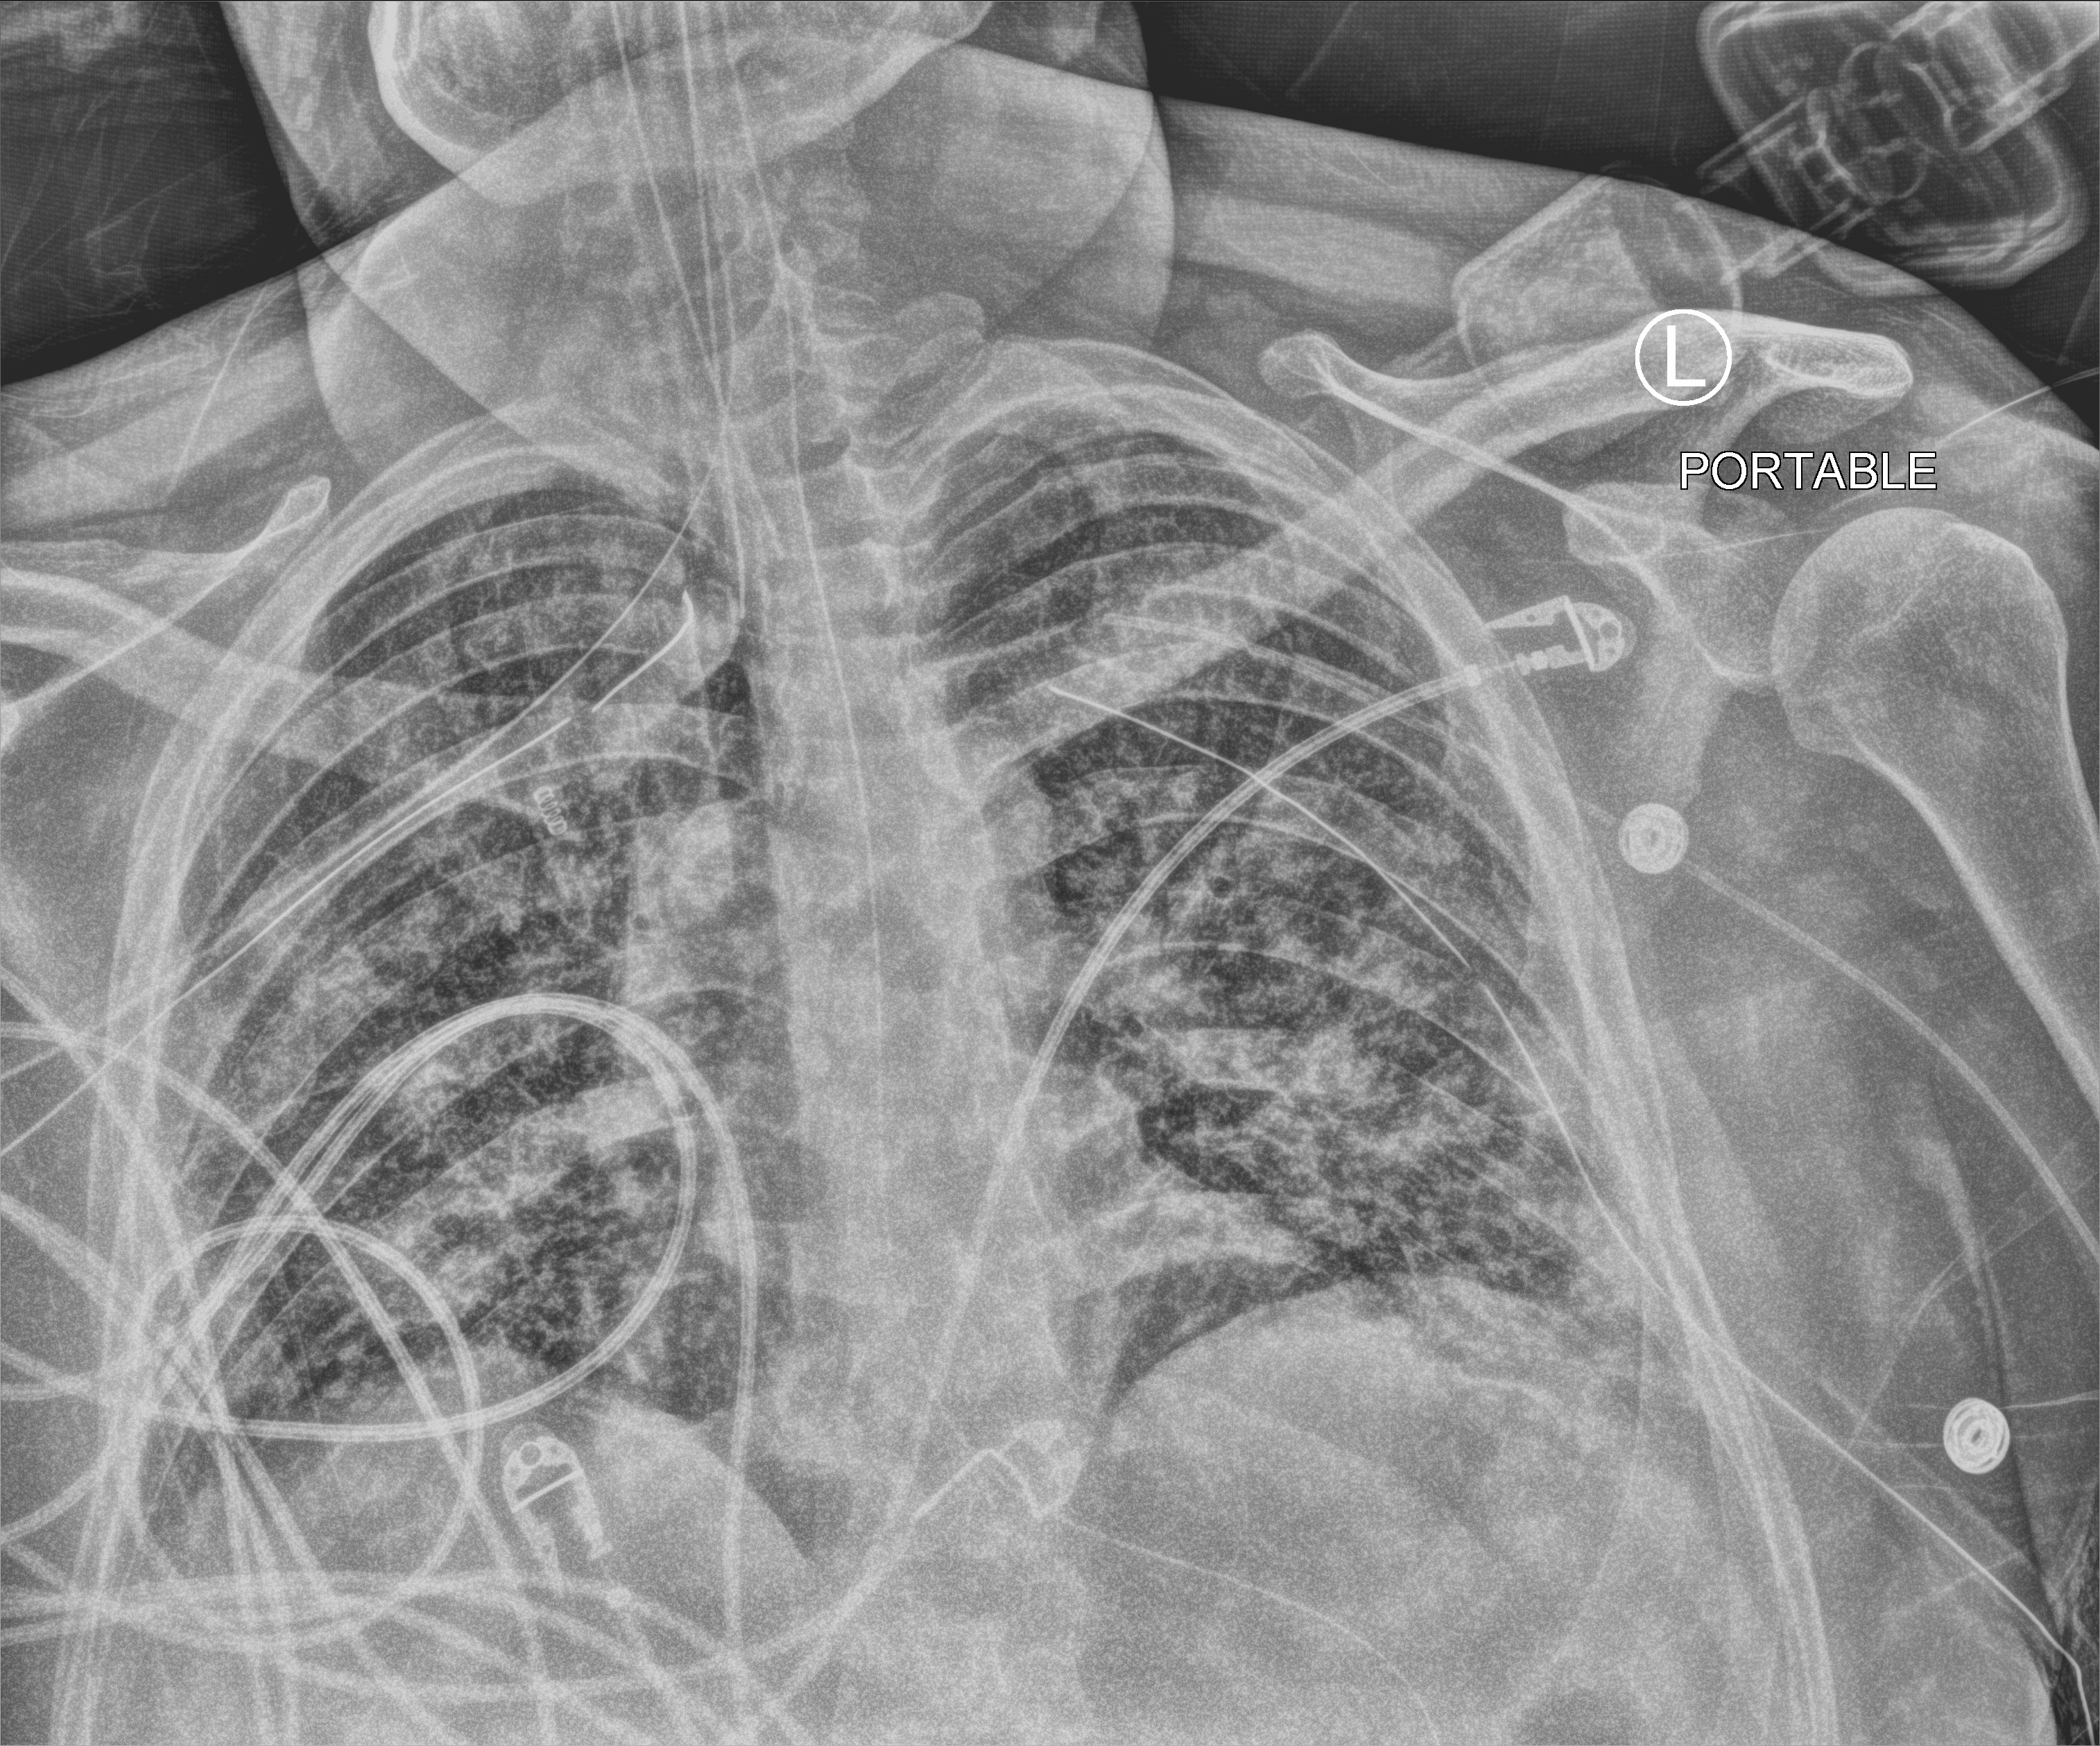
Chest X-ray (portable); anteroposterior (AP) projection. Male patient hospitalised with COVID-19, age 18–59 years.
Hospital-stay facts (about this admission, not read from this image; timing relative to this image not recorded): length of hospital stay: 63 days; mechanically ventilated during this hospital stay: yes; admitted to intensive care during this hospital stay: yes.